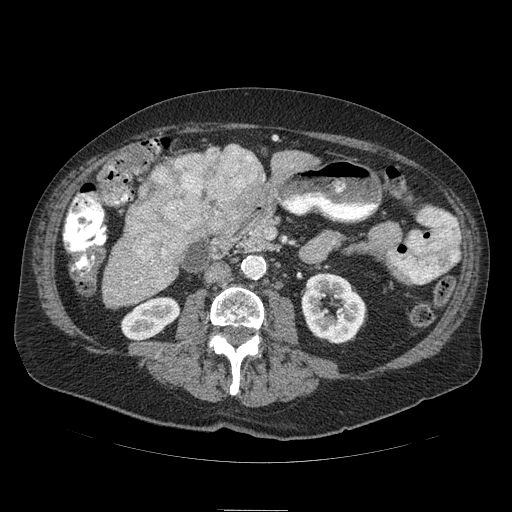
Contrast-enhanced abdominal CT (liver protocol), one axial slice. Slice 23 of 103 in the series (ordered by position). Reconstruction kernel STANDARD. 120 kVp. Soft-tissue window (W 400 / L 40 HU). 2.5 mm slice thickness. 512 × 512 image matrix. From the clinical record (not read from this slice): diagnosis: hepatocellular carcinoma (patient treated with transarterial chemoembolisation; whether this scan precedes or follows treatment is not stated here); TNM stage (as recorded): Stage-IIIA; Child-Pugh class: B; tumour differentiation: well differentiated; tumour nodularity: multinodular.
Annotated regions visible in this slice (semi-automatic segmentation, software-assisted and operator-edited):
- liver parenchyma outside the tumour (the mass and vessels are separate outlines, so this box may not span the whole liver): box from (x=112, y=144) to (x=317, y=268) px
- mass: (x=126, y=144)–(x=271, y=268)